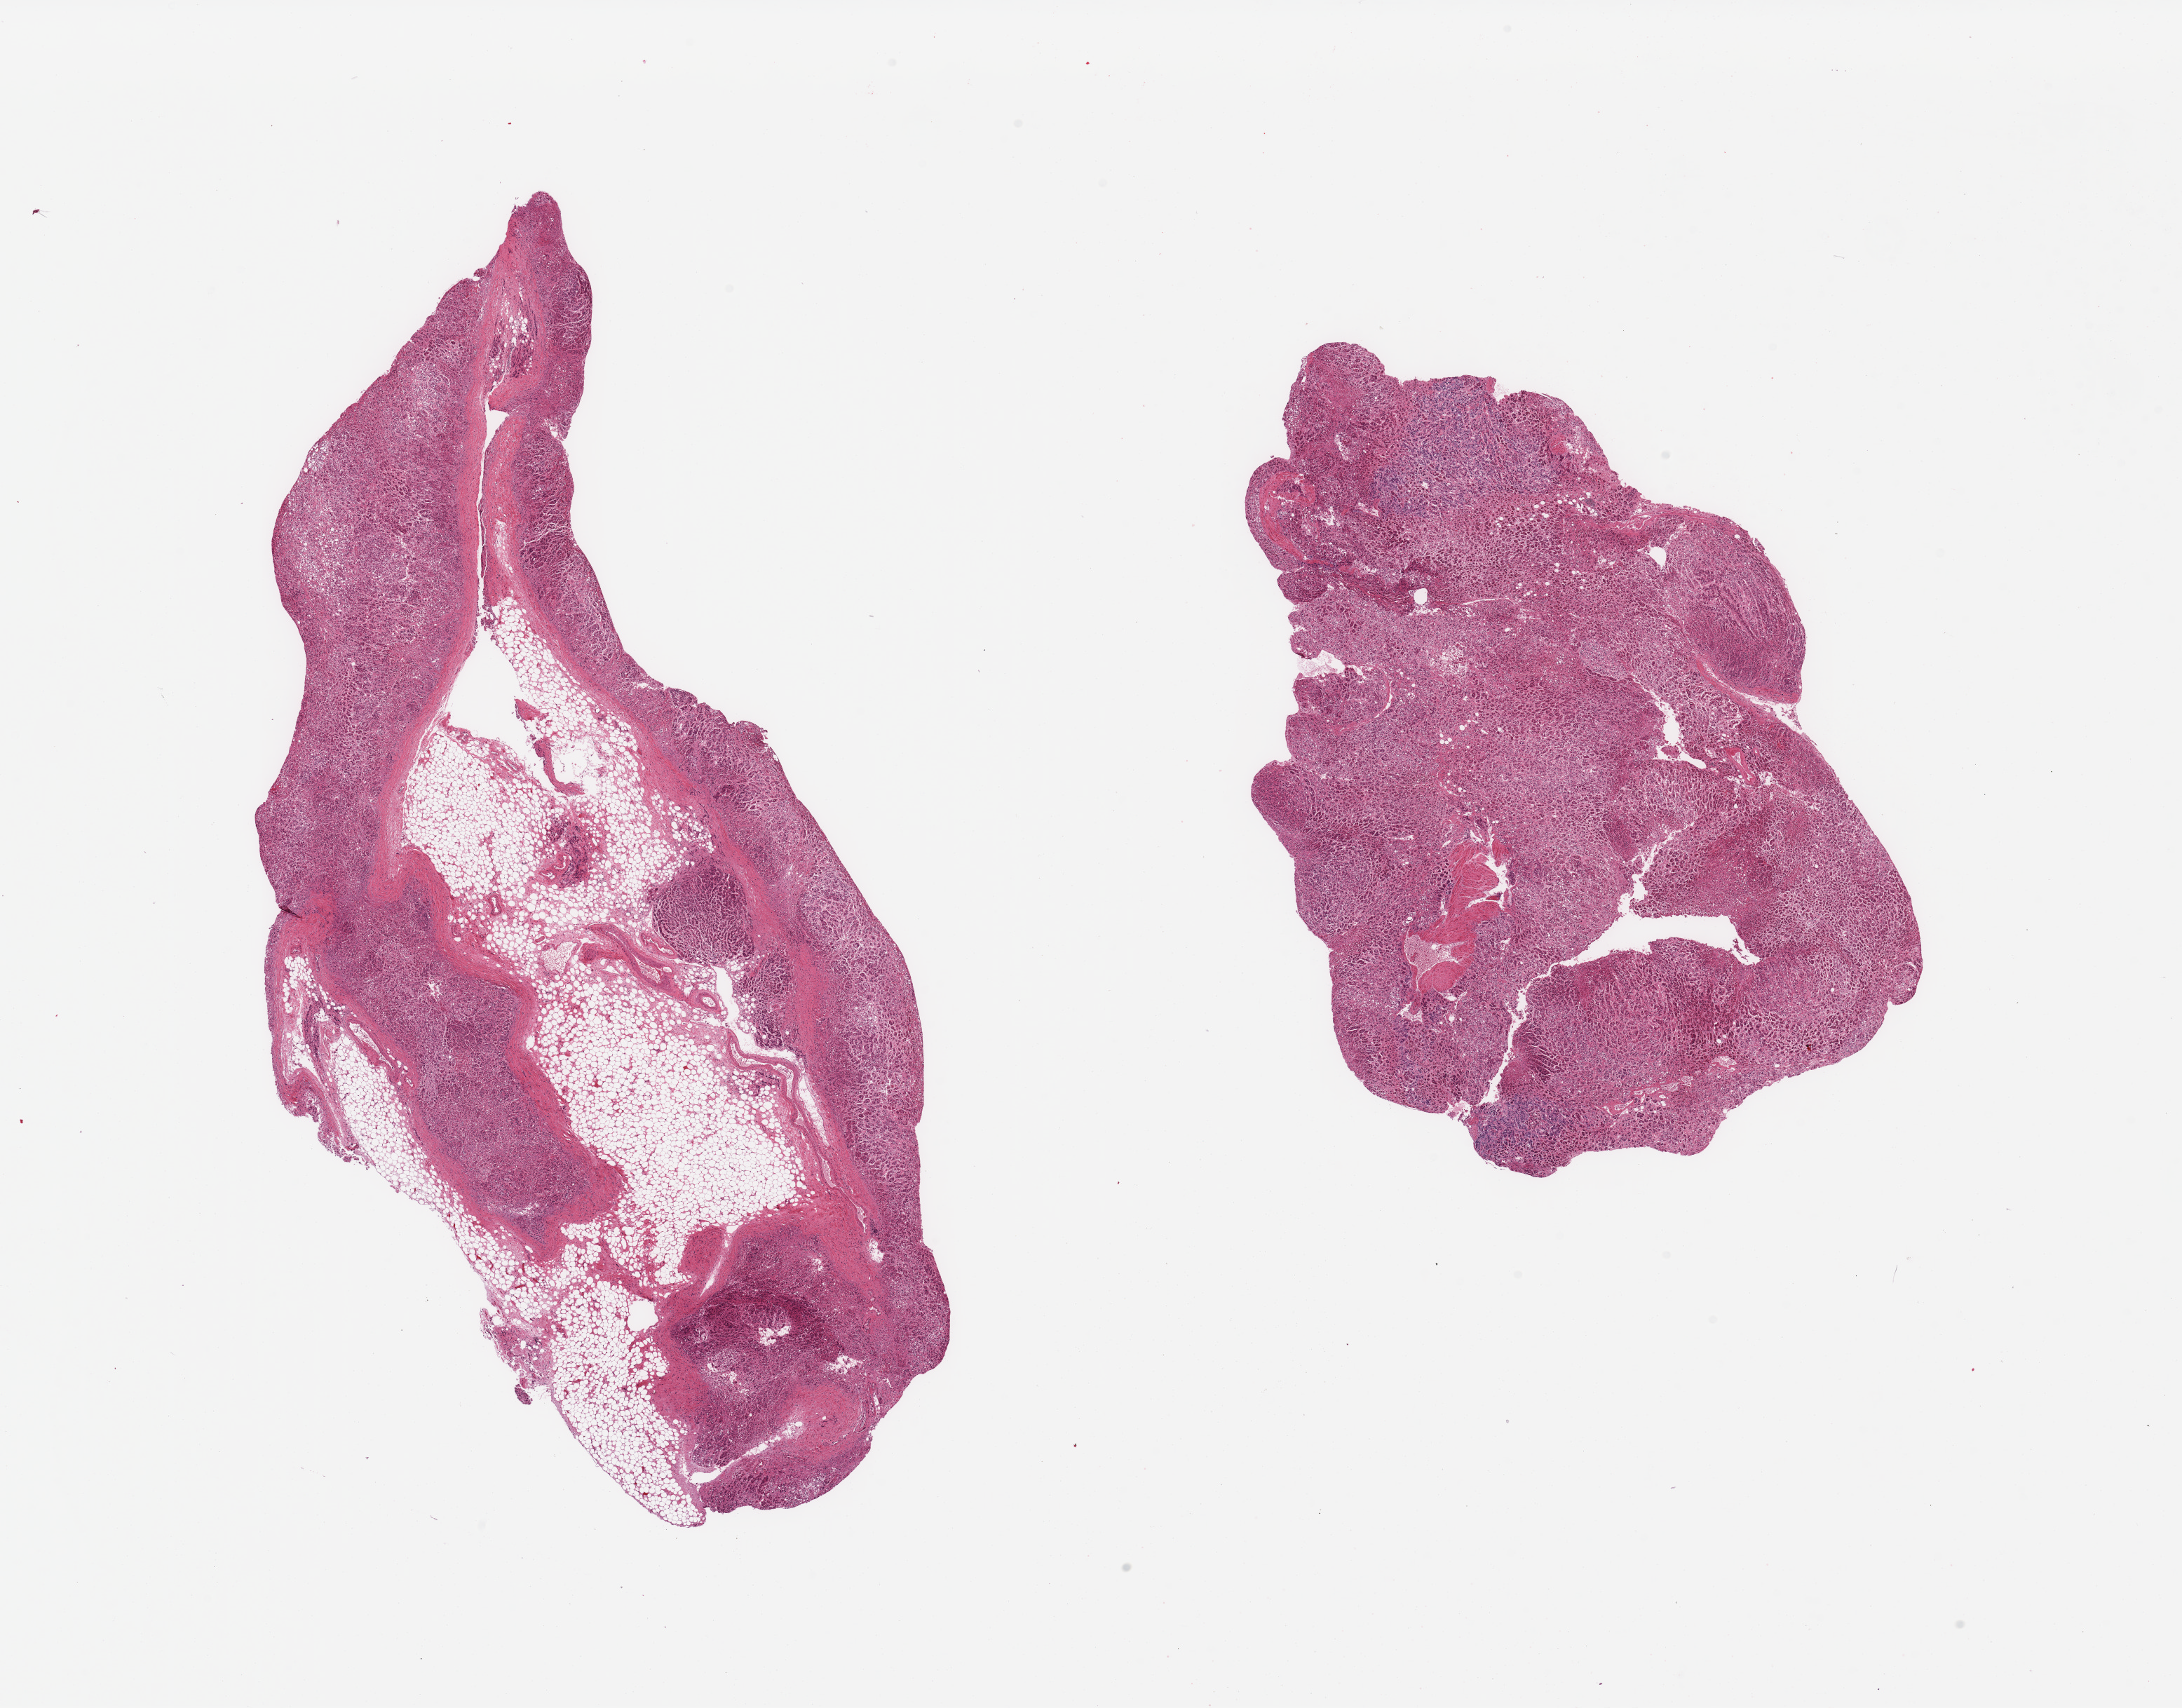
H&E whole-slide image, brightfield — a low-resolution overview of the entire scanned area, about 24.6 x 19.3 mm (from a 20x scan). PAXgene-fixed paraffin-embedded (PFPE) section. Sampled site (target tissue): adrenal gland. Donor tissue sample. Donor sex: female.
* review note (as recorded): 2 pieces; 1 piece with 60% fat content; other free of fat